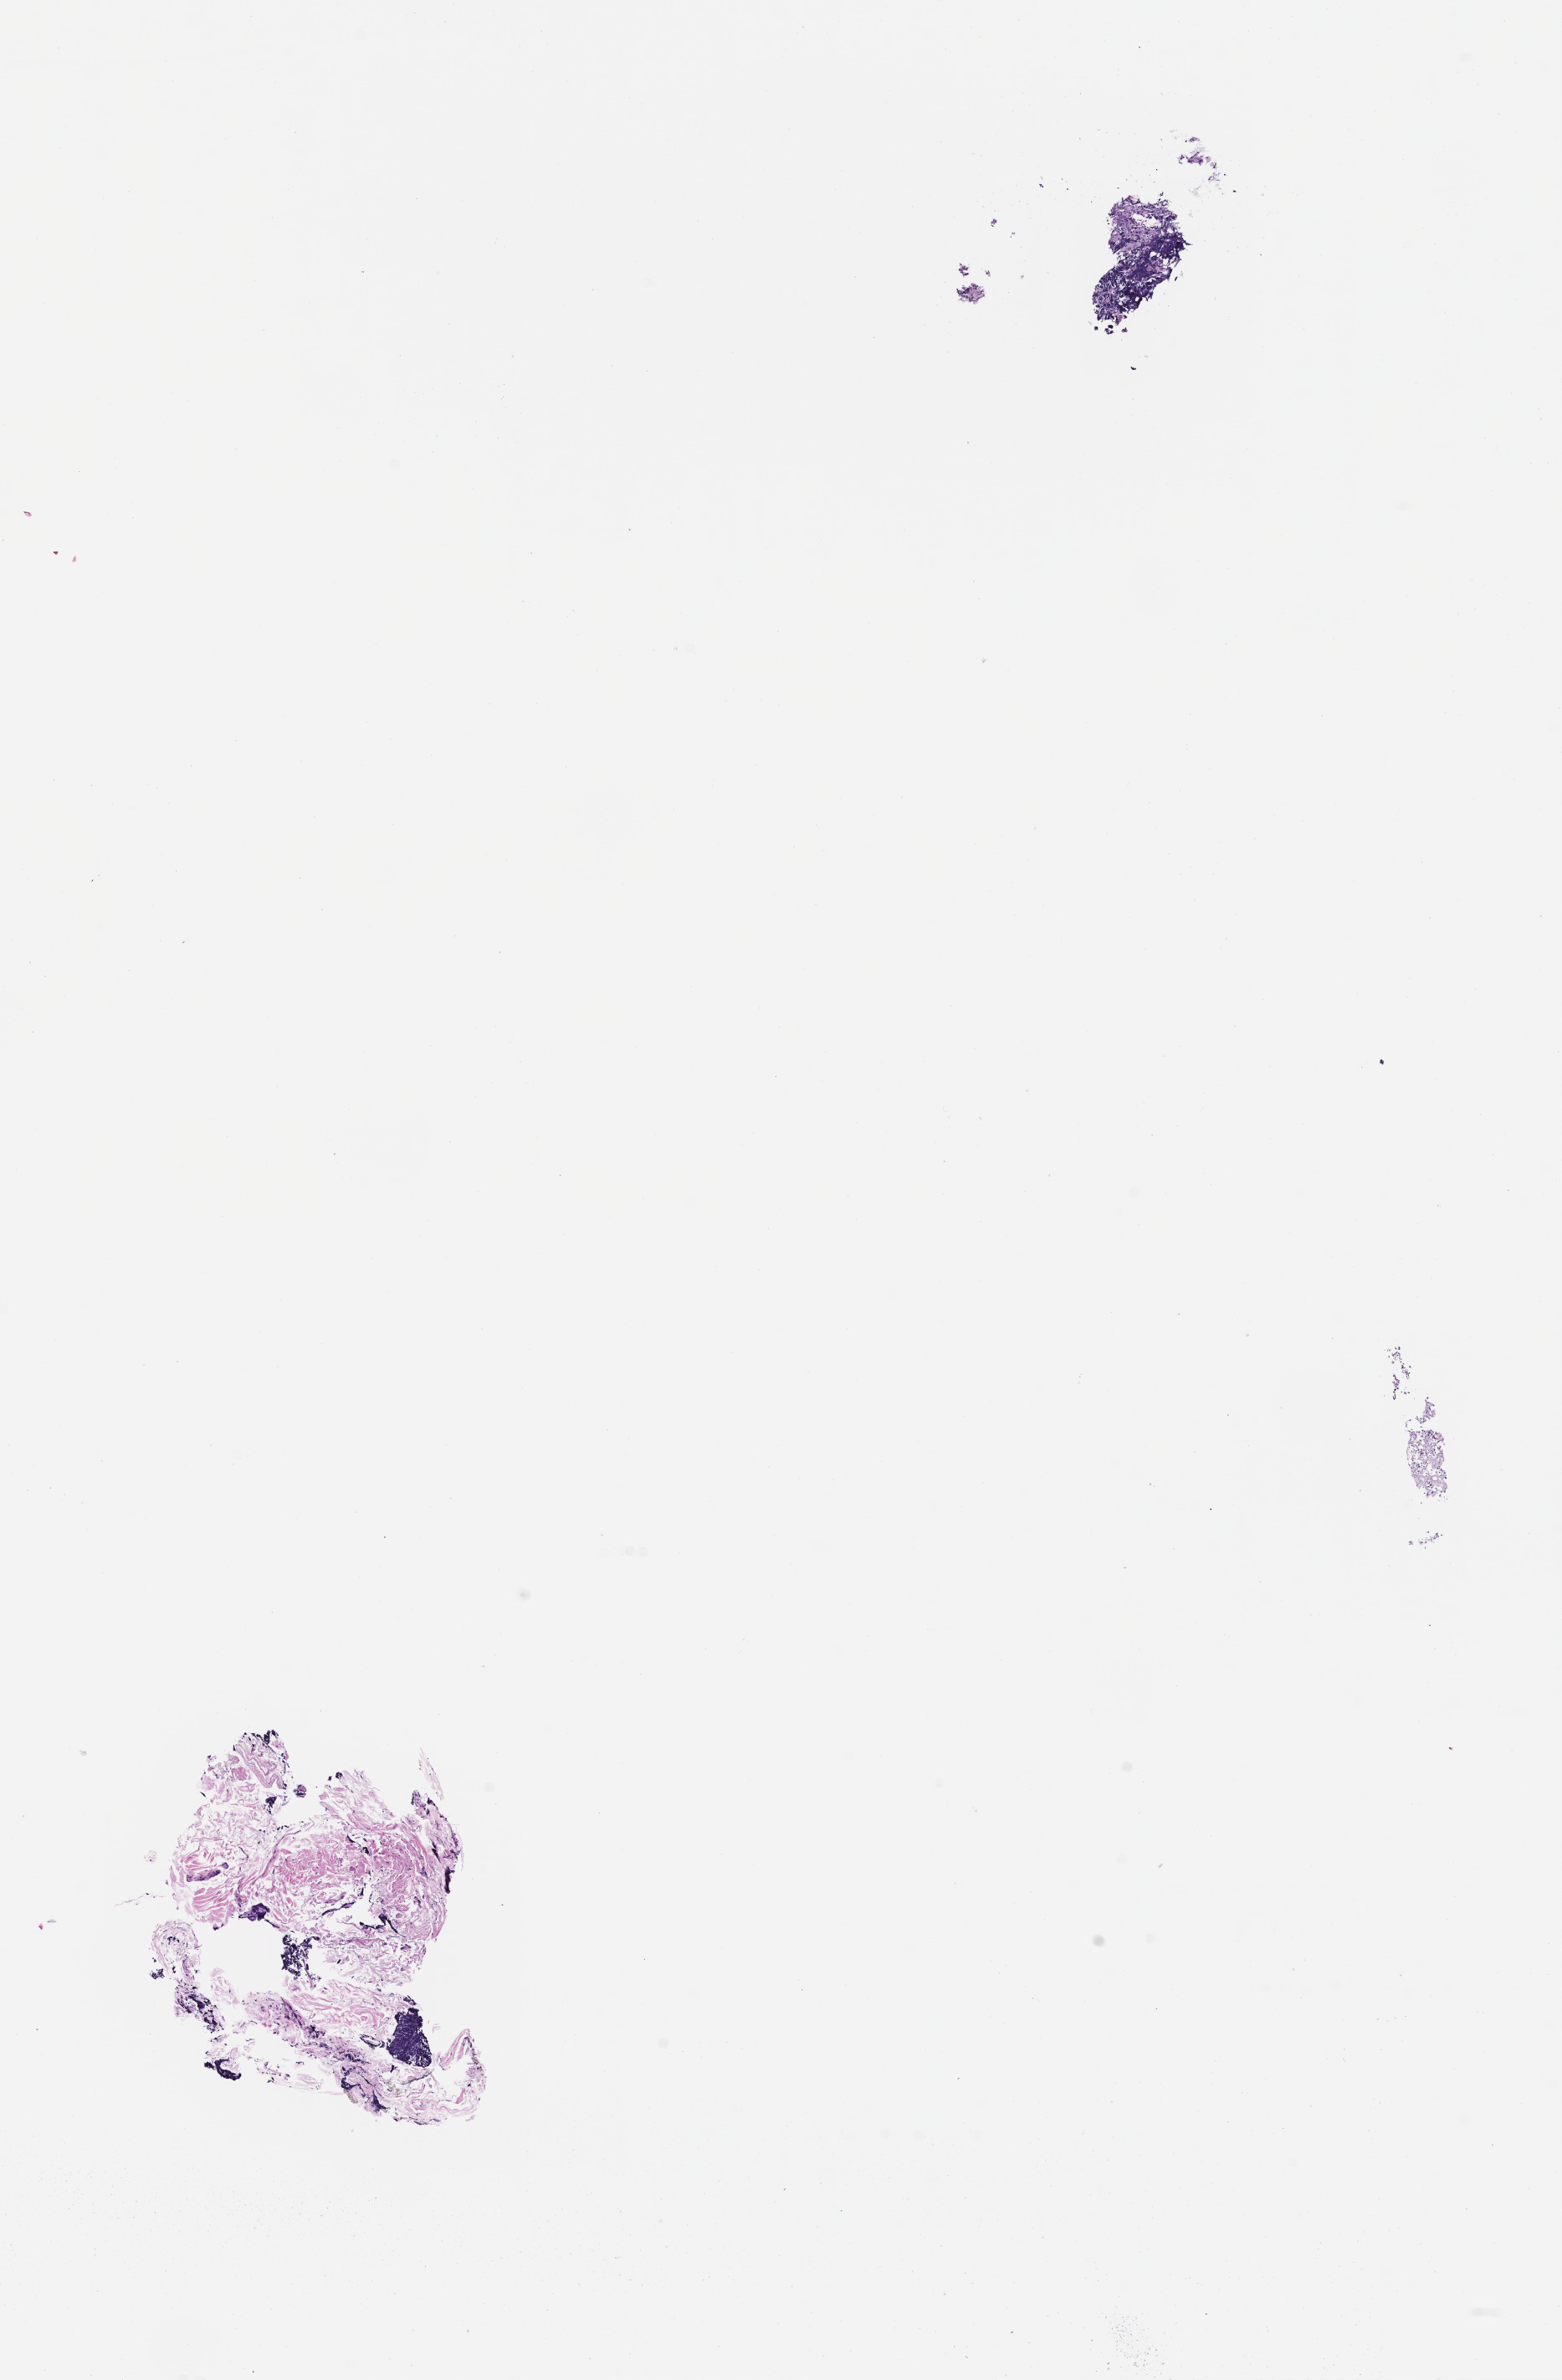
Whole-slide image, H&E stain — a low-resolution overview of the entire scanned area, about 7.5 x 11.5 mm. Formalin-fixed, paraffin-embedded (FFPE) tissue. Patient sex: male.
This section: metastatic tumor tissue. Patient diagnosis (primary): Small Cell Lung Carcinoma.